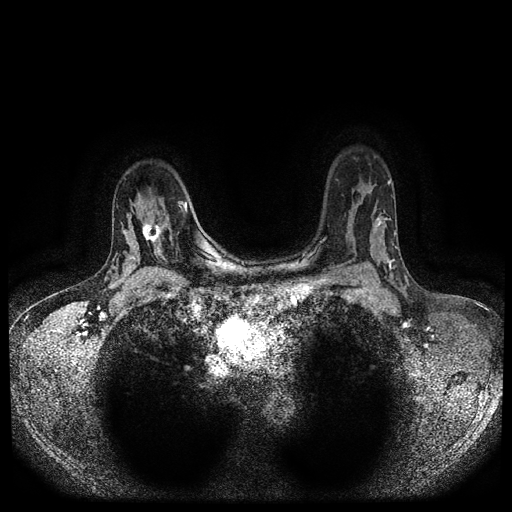
Breast MRI (dynamic contrast-enhanced, multi-phase), one axial slice; slice 72 of 116 in the series (ordered by position); dynamic contrast-enhanced series, time point 2 of 5 at this slice position (early post-contrast); 1.5 T; TE 2.6 ms, TR 5.4 ms; 2 mm slice thickness; 512 × 512 image matrix, field of view 340 × 340 mm. Female patient, age 47 years.
Outlined on this slice (semi-automatic segmentation, software-assisted and operator-edited):
- breast lesion (labelled 'tumour' in the annotation; benign lesions carry a separate 'benign' label): bounding box [x1, y1, x2, y2] px = [140, 218, 164, 246]